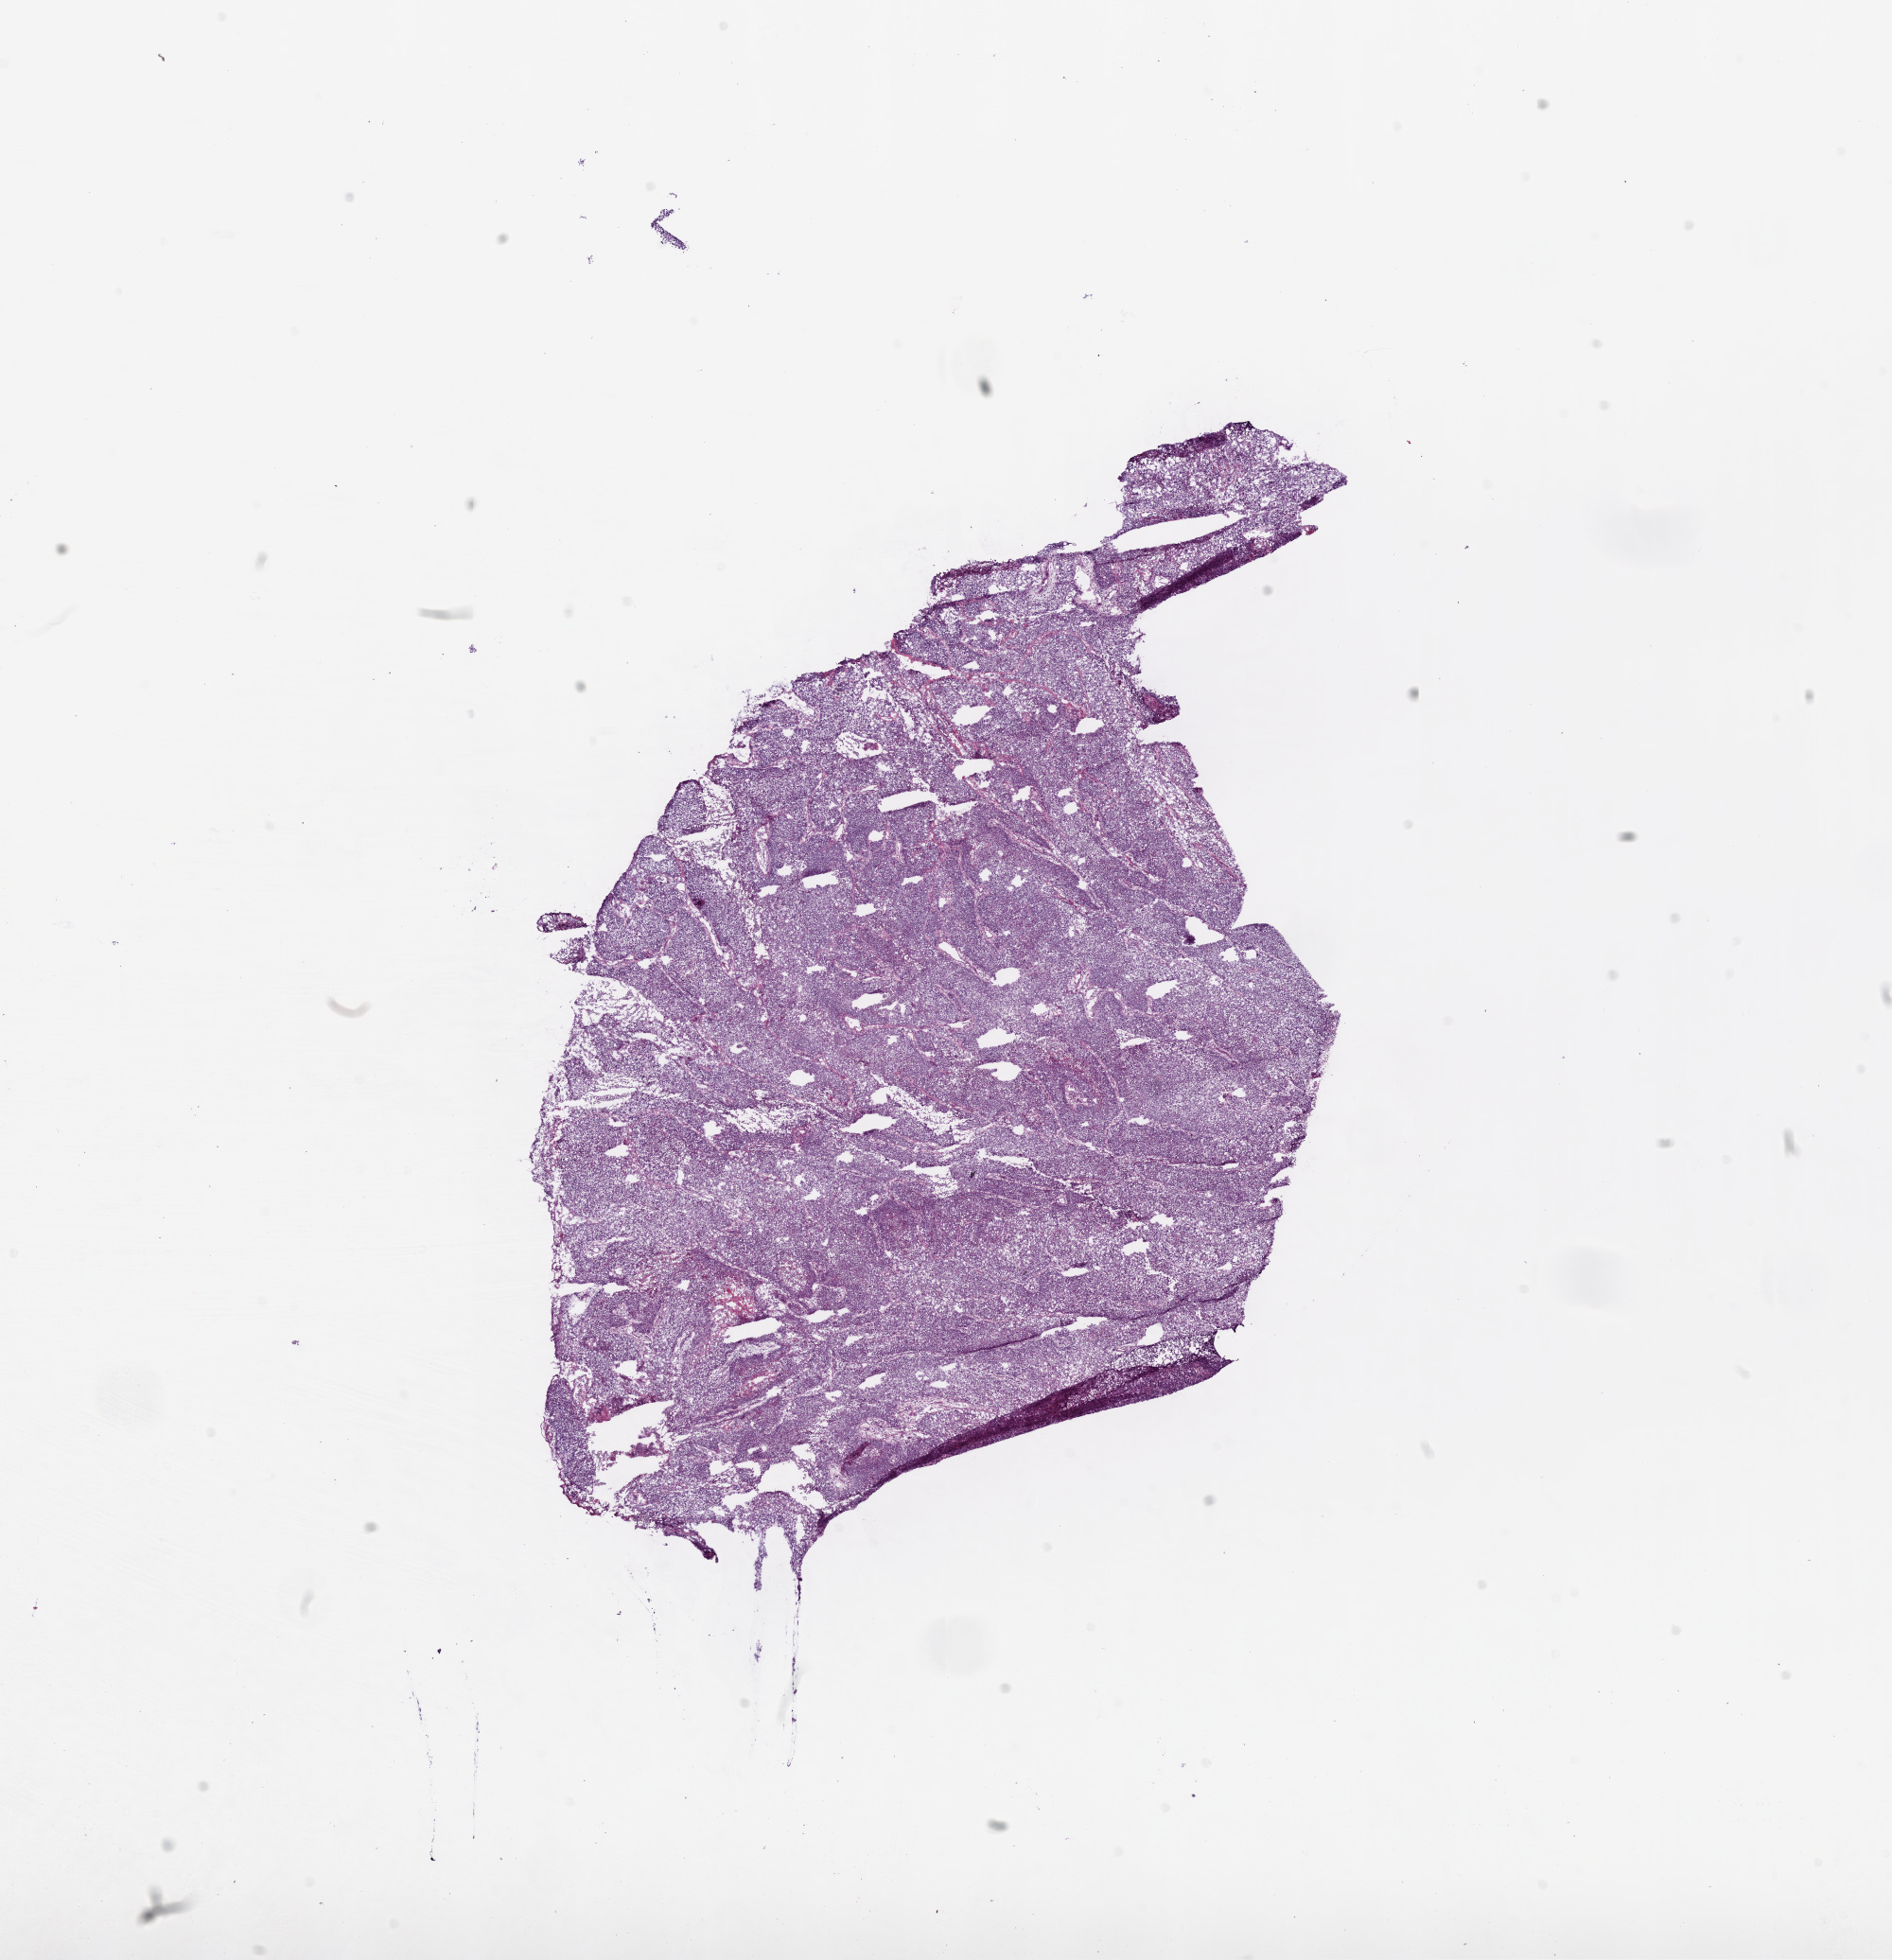
Whole-slide histology image, H&E — whole scanned area (about 16.0 x 16.6 mm, slide scanned at 20x) shown as a low-resolution overview. Frozen section. Primary tumour sample from the lung. Male patient; age at initial diagnosis 57 years. Slide review estimates, as recorded: tumour cells 90%, tumour nuclei 90%, normal cells 0%, stromal cells 5%, necrosis 5%.
Diagnosis: Squamous cell carcinoma, NOS. AJCC pathologic stage: IIB (6th edition).